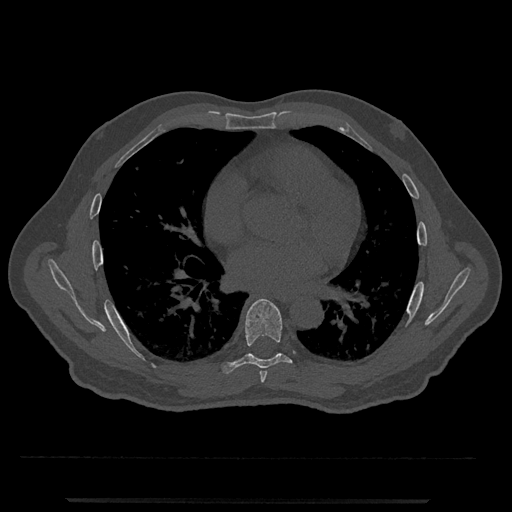
CT including the spine, one axial slice; position 685 of 797 along the scan axis; 120 kVp; bone window (W 1800 / L 400 HU); 0.5 mm slice thickness; 512 × 512 image matrix. Patient: male, 63 years. From the clinical record (not read from this slice): primary cancer: prostate.
Outlined on this slice (semi-automatic segmentation, software-assisted and operator-edited):
- T6 vertebra: bounding box <259,371,267,383> (left, top, right, bottom; pixels)
- T7 vertebra: <220,299,293,375>